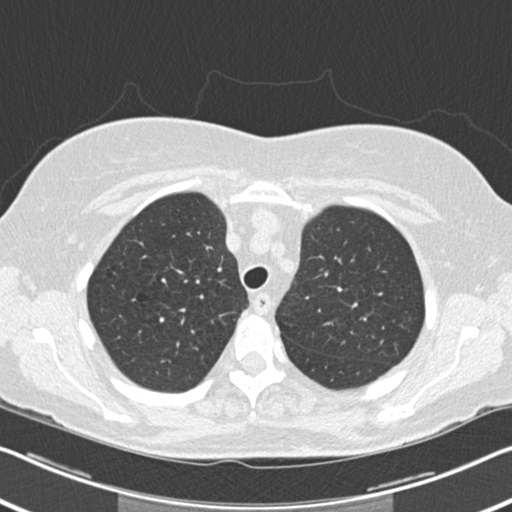
Chest CT (low-dose screening protocol), one axial image. Second screening round (one year after baseline). Lung window (W 1500 / L -600 HU). 2 mm slice thickness. Slice 49 of 202 in the series. Female participant, aged 60 years at enrolment. Current smoker at enrolment.
Lesion marked by an expert reader, bounding box <387,304,424,343> (left, top, right, bottom; pixels). The screening reader recorded 6 non-calcified nodules or masses ≥4 mm on this exam (right upper lobe, right middle lobe, right lower lobe, right lower lobe, left lower lobe, lingula); which of them this box marks is not recorded. Official screen result: positive, change unspecified: nodule(s) >= 4 mm or enlarging nodule(s), mass(es), or other non-specific abnormalities suspicious for lung cancer. Participant outcome: lung cancer diagnosed 495 days after this screen — non-small cell carcinoma, left upper lobe, poorly differentiated (G3), stage IB (AJCC 6th edition), 7 mm at pathology.